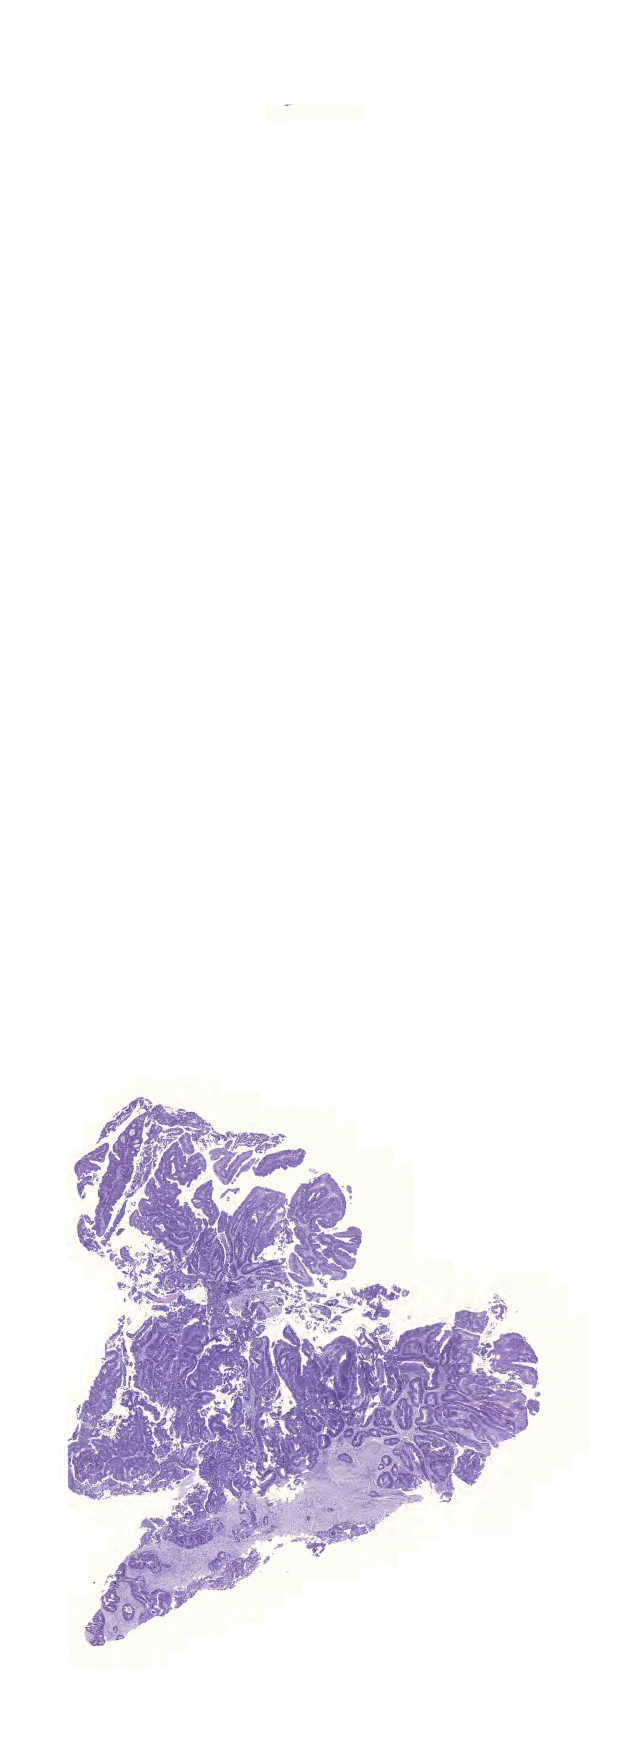
Whole-slide histology image, Hematoxylin and eosin (H&E) stained — whole scanned area (about 9.6 x 26.2 mm, acquisition: 20x scan) shown as a low-resolution overview. FFPE section. Primary tumour sample from the colon. Patient: male, age at initial diagnosis 38 years.
Lymph nodes positive (case pathology): 5 of 31 examined. Diagnosis: Adenocarcinoma, NOS. AJCC pathologic stage: IIIB (7th edition).